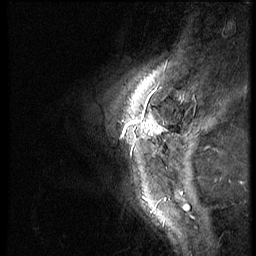
Breast MRI (dynamic contrast-enhanced), one sagittal slice. Position 12 of 56 along the scan axis. Dynamic contrast-enhanced series, image 2 of 3 at this slice position (ordered by acquisition). 1.5 T. TE 4.2 ms, TR 9 ms. 2.5 mm slice thickness. 256 × 256 image matrix. Female patient, age 46 years. Case-level facts recorded for this patient, not image findings: setting: breast cancer imaged before/during neoadjuvant chemotherapy; receptor status: HER2-positive.
Outlined on this slice (semi-automatically segmented with operator editing):
- analysis volume of interest (the breast-tissue region the enhancement analysis was run in; not a lesion): box from (x=86, y=98) to (x=174, y=182) px
- tumour enhancement mask (voxels above the 140 % enhancement threshold inside the analysis volume of interest): (x=122, y=121)–(x=157, y=137)